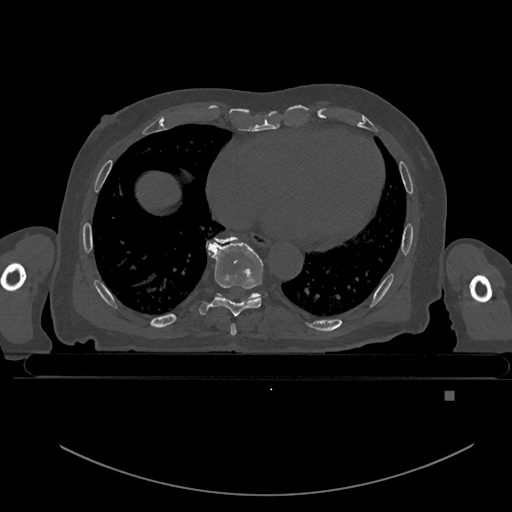
CT including the spine, one axial slice; bone window (W 1800 / L 400 HU); 0.5 mm slice thickness; 512 × 512 image matrix. Patient: male, 82 years. Case-level facts recorded for this patient, not image findings: primary cancer: prostate; vertebrae with lytic lesions (as recorded): T11, T9, T8, T2.
Outlined on this slice (semi-automatic segmentation, software-assisted and operator-edited):
- T7 vertebra: bounding box [x1, y1, x2, y2] px = [230, 324, 236, 336]
- T8 vertebra: [199, 238, 263, 317]
- T9 vertebra: [216, 237, 261, 300]